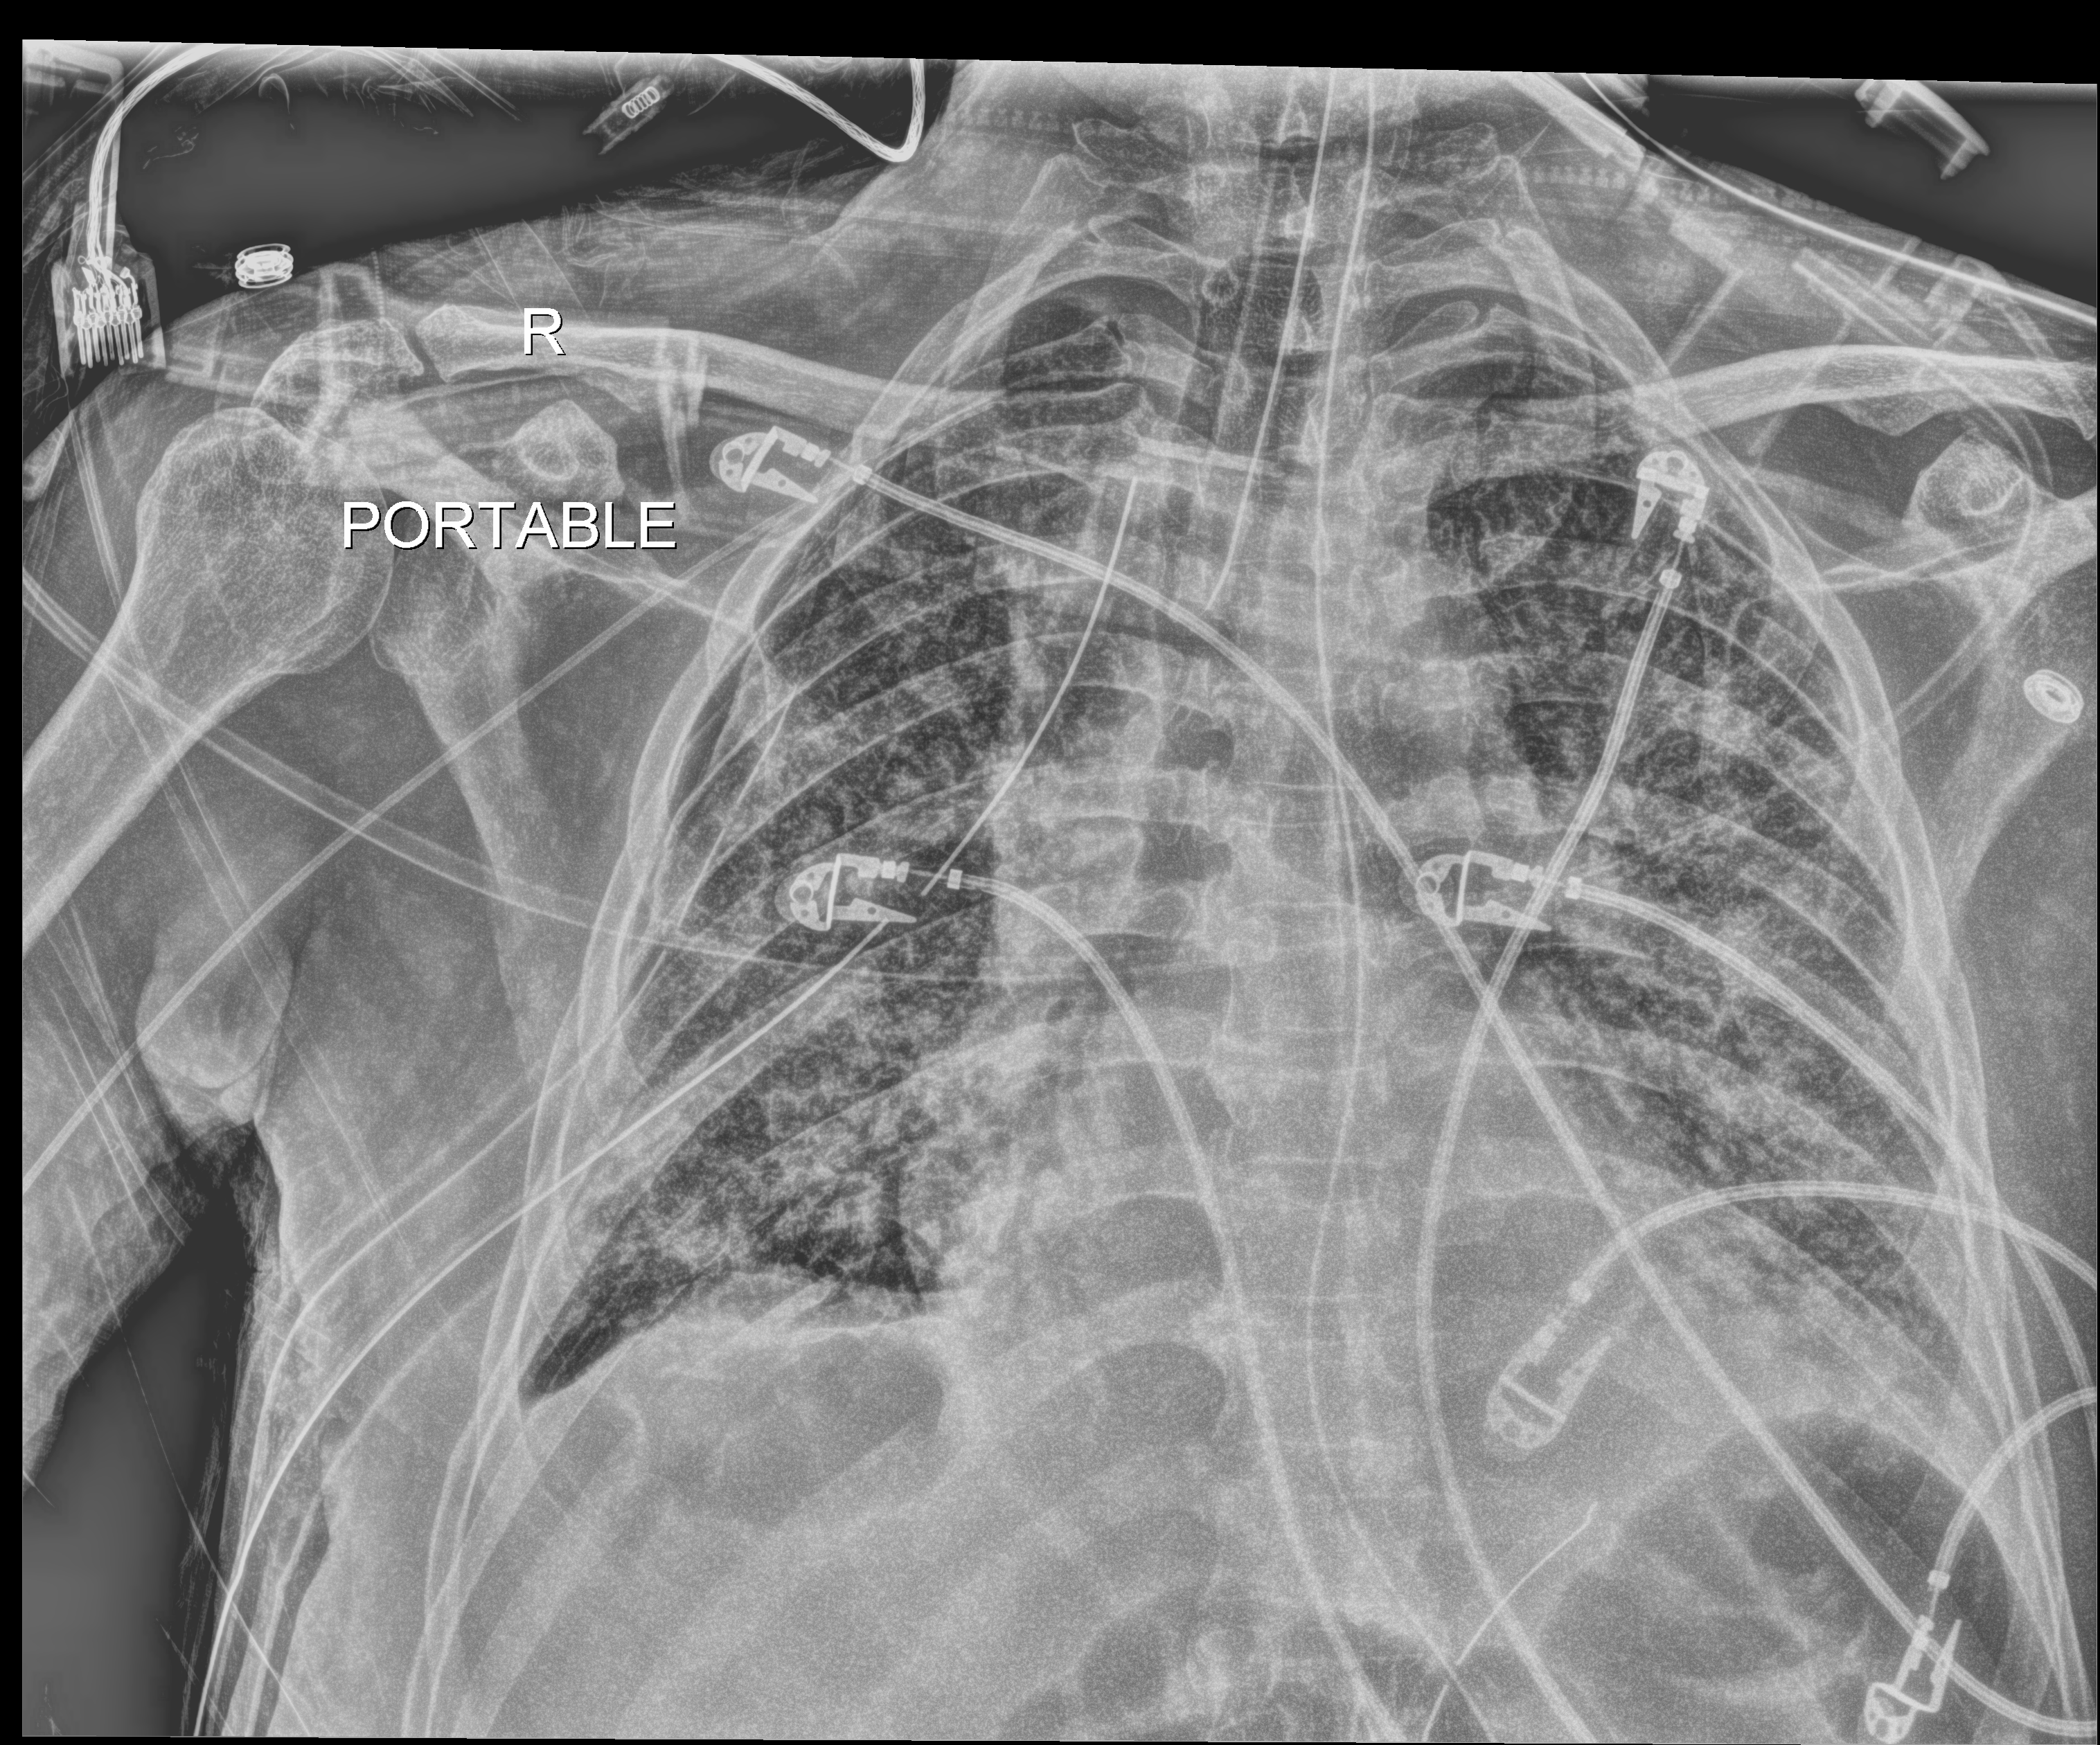
Bedside chest radiograph (digital radiography); anteroposterior (AP) projection. Patient hospitalised with COVID-19; male, aged 60–74 years.
Admission-level facts for this patient (not findings on this image; timing relative to this image not recorded): admitted to intensive care during this hospital stay: yes; mechanically ventilated during this hospital stay: yes.